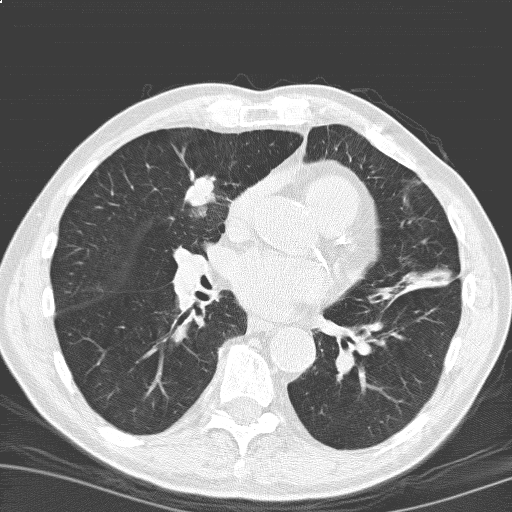
Low-dose screening chest CT, one axial slice; slice 91 of 184 in the series (ordered by position); 120 kVp; lung window (W 1500 / L -600 HU); 512 × 512 image matrix.
Structures marked on this image (outlined manually by an expert reader):
- lesion 1 (tumor, upper lobe of right lung): bounding box <185,176,216,216> (left, top, right, bottom; pixels)